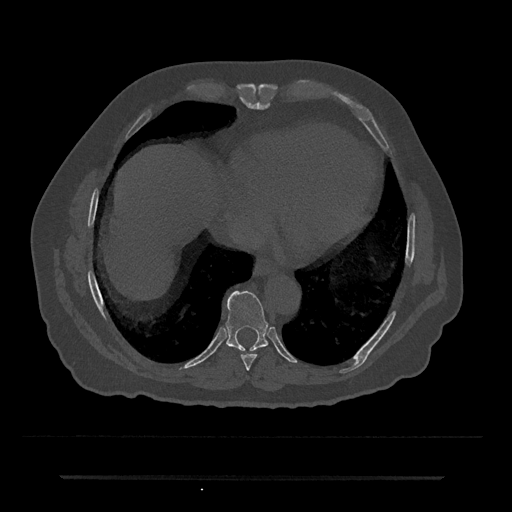
CT including the spine, one axial slice. Slice 299 of 797 in the series (ordered by position). Reconstruction kernel Br40s/3. 120 kVp. Bone window (W 1800 / L 400 HU). 512 × 512 image matrix, field of view 437 × 437 mm. Male patient, age 69 years. From the clinical record (not read from this slice): primary cancer: prostate.
Outlined on this slice (semi-automatic segmentation, software-assisted and operator-edited):
- T8 vertebra: box from (x=241, y=354) to (x=257, y=370) px
- T9 vertebra: (x=226, y=291)–(x=268, y=351)